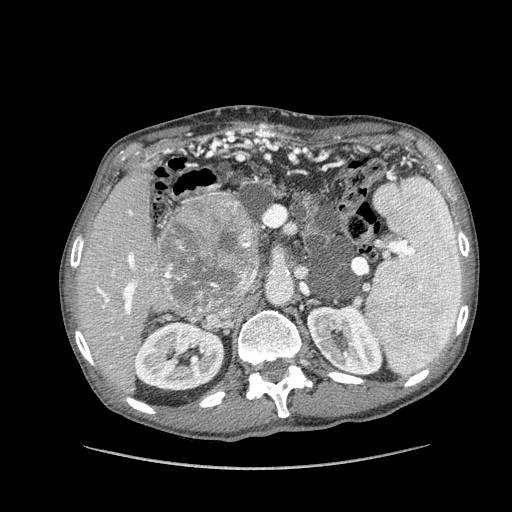
Contrast-enhanced abdominal CT (liver protocol), one axial slice; slice 67 of 162 in the series (ordered by position); reconstruction kernel STANDARD; 100 kVp; soft-tissue window (W 400 / L 40 HU); 512 × 512 image matrix, field of view 400 × 400 mm. From the clinical record (not read from this slice): diagnosis: hepatocellular carcinoma (patient treated with transarterial chemoembolisation; whether this scan precedes or follows treatment is not stated here); TNM stage (as recorded): Stage-IIIA; Child-Pugh class: A; tumour nodularity: multinodular; tumour size: 9.9 cm.
Outlined on this slice (semi-automatic segmentation, software-assisted and operator-edited):
- liver parenchyma outside the tumour (the mass and vessels are separate outlines, so this box may not span the whole liver): bounding box (x1, y1, x2, y2) in pixels: (78, 164, 262, 390)
- mass: (156, 197, 261, 313)
- liver vessels: (96, 211, 154, 340)